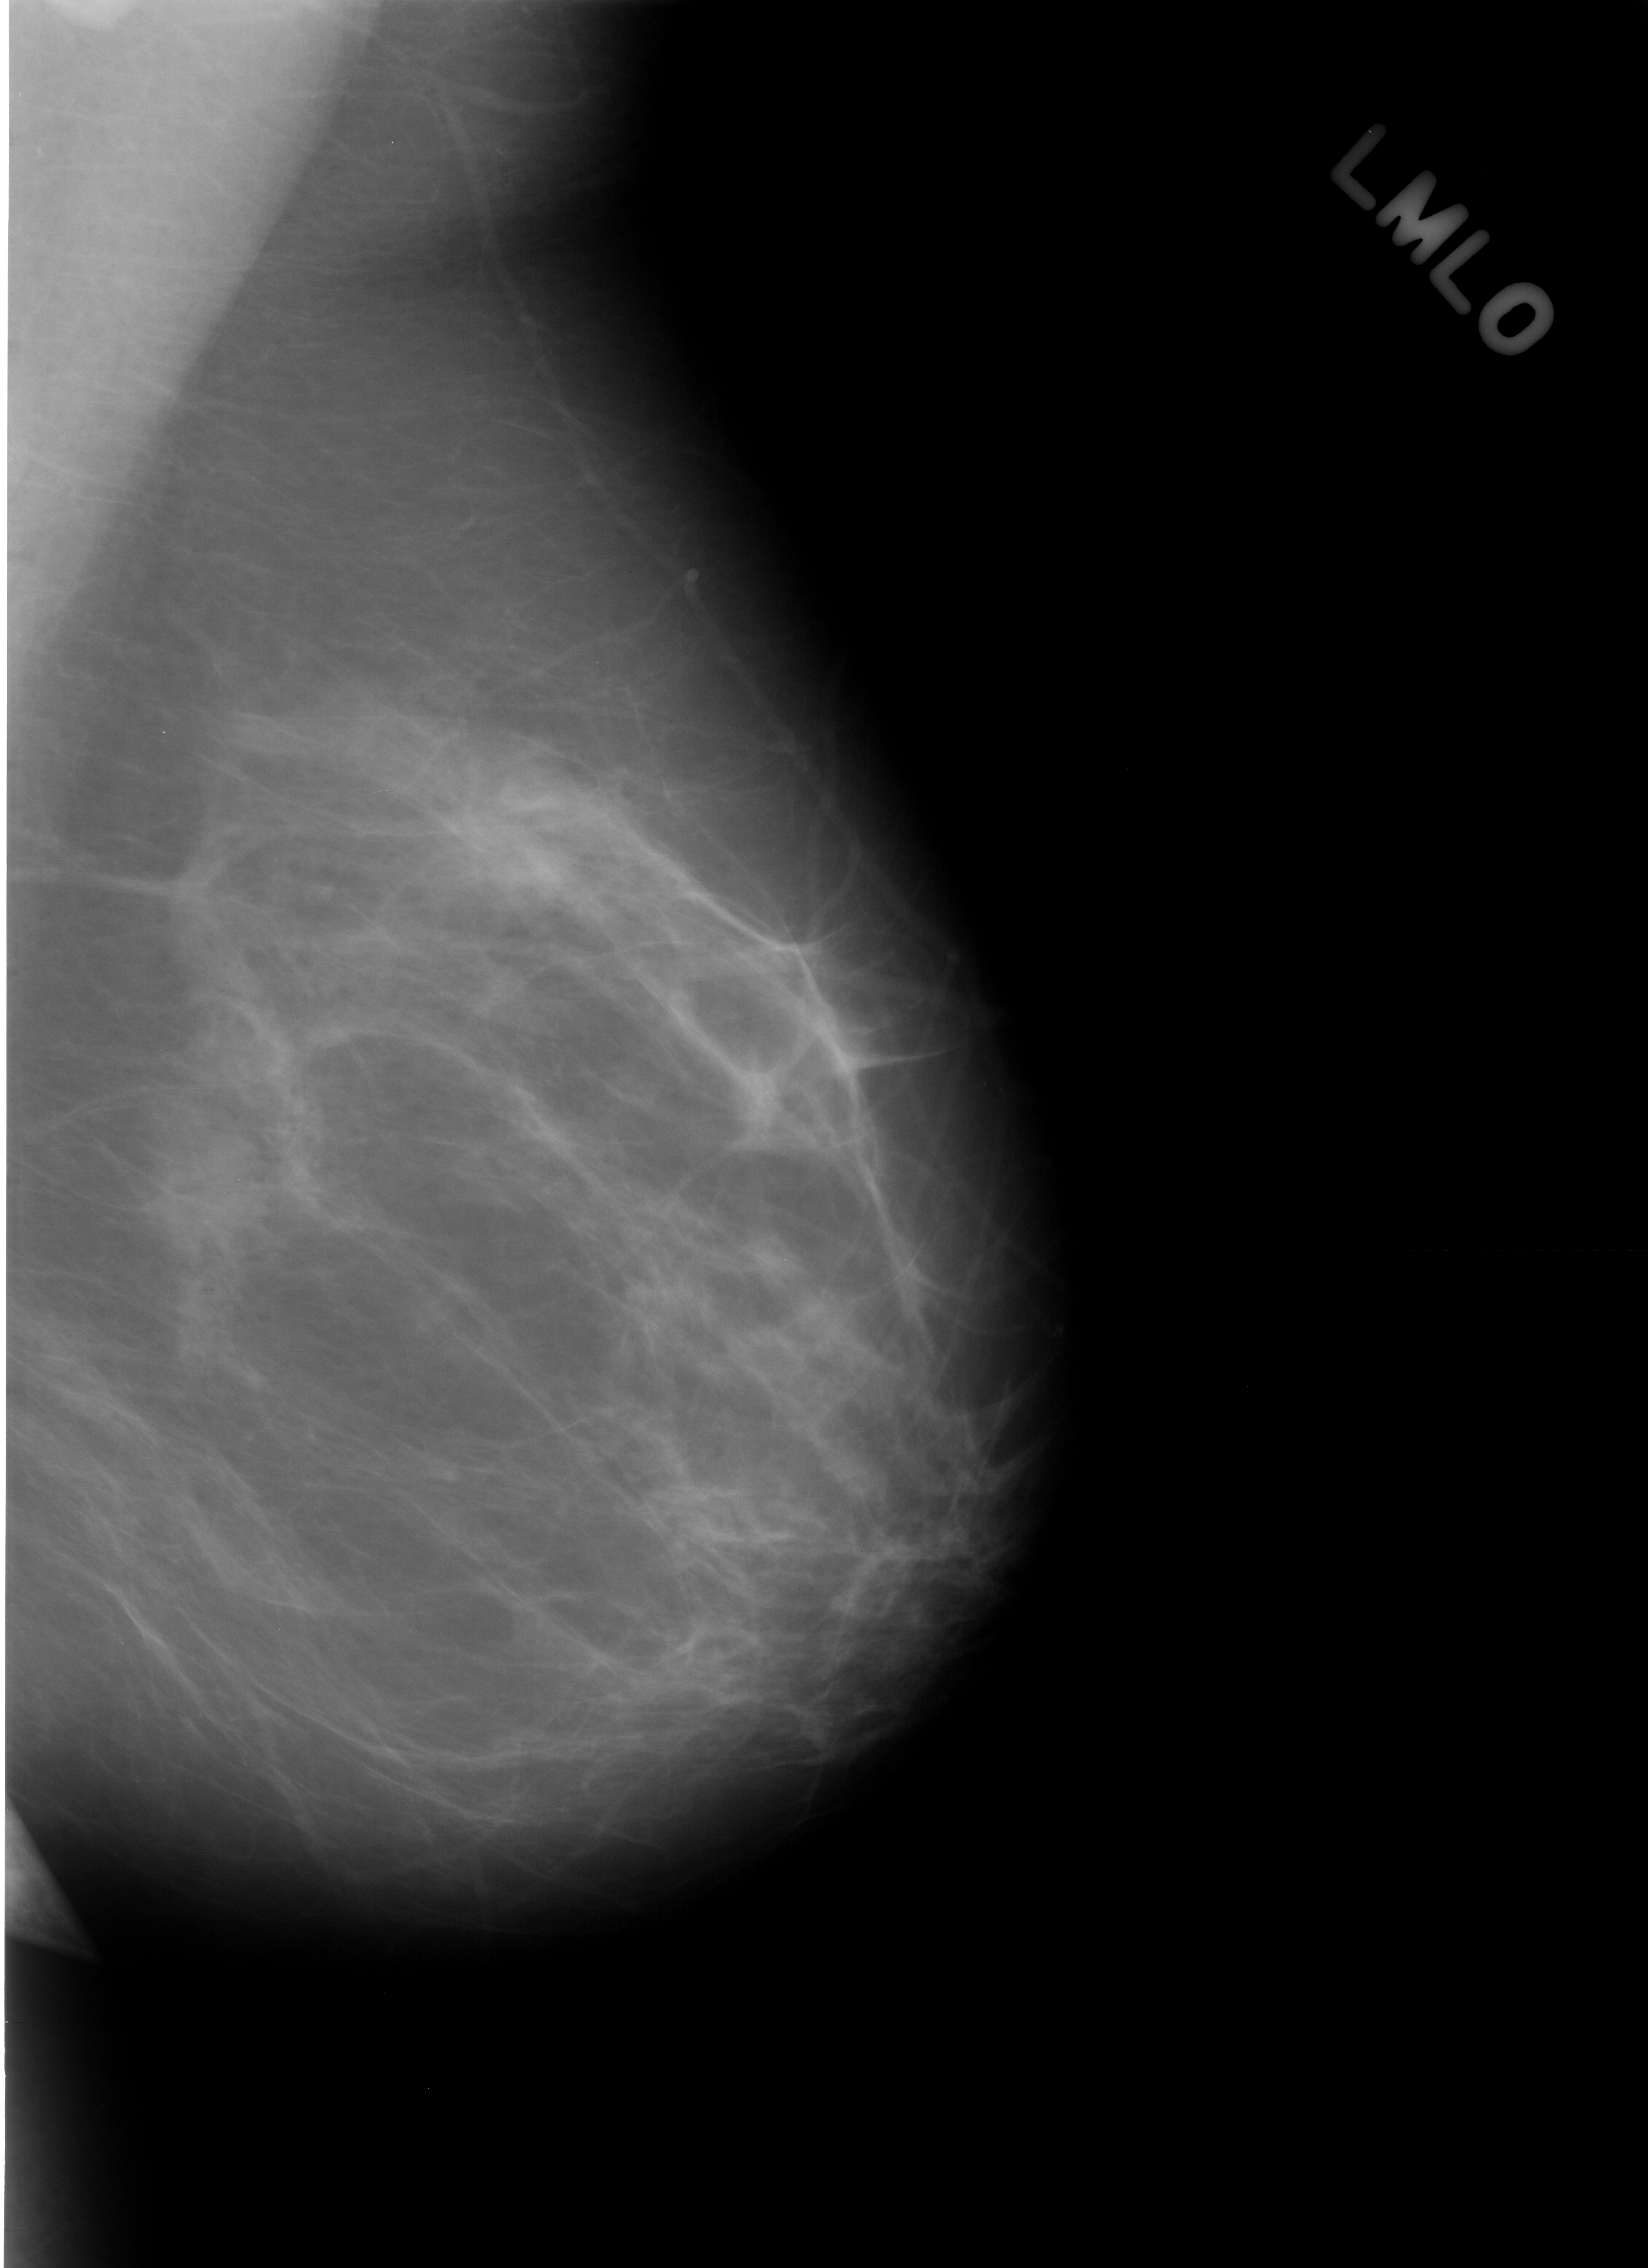
Mammogram (digitized film). Left breast. MLO view. BI-RADS breast density category 1 (scale 1–4). 1648 × 2268 image matrix.
Expert-marked regions of interest on this film, with their recorded descriptors:
- mass, shape irregular, margins spiculated; BI-RADS assessment category 3; outcome (as recorded, no biopsy): benign without callback (not worked up further): bounding box <133,1103,265,1253> (left, top, right, bottom; pixels)